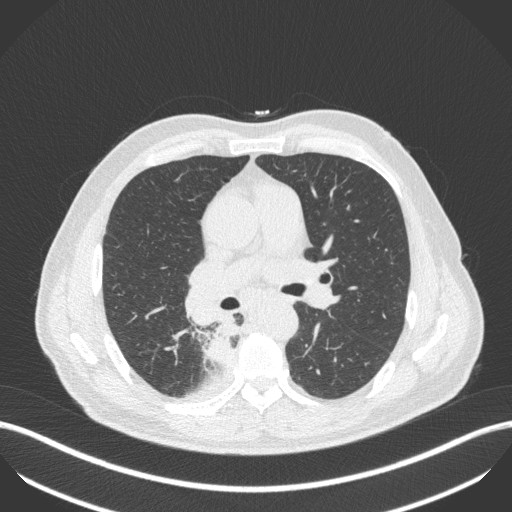
Chest CT, one axial slice. Slice 270 of 451 in the series (ordered by position). Reconstruction kernel B31f. 100 kVp. Lung window (W 1500 / L -600 HU). 512 × 512 image matrix, field of view 400 × 400 mm. Male patient, age 61 years. From the clinical record (not read from this slice): clinical TNM (as recorded): T1 N0 M0; histopathological grade: G3.
Structures marked on this image (bounding box drawn by a radiologist):
- lung tumour (recorded histology: small cell carcinoma): box from (x=204, y=321) to (x=243, y=367) px